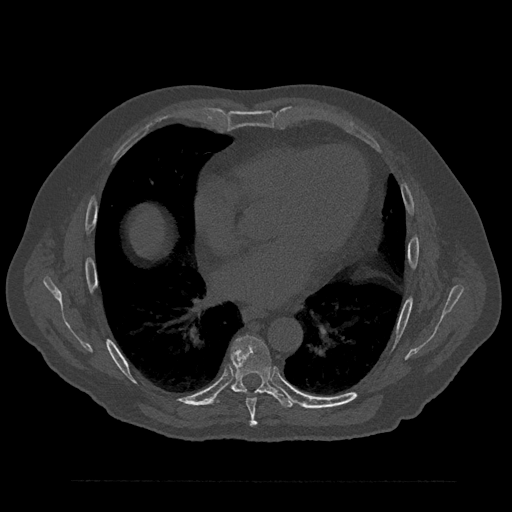
CT including the spine, one axial slice; slice 477 of 797 in the series (ordered by position); 120 kVp; bone window (W 1800 / L 400 HU); 0.5 mm slice thickness; 512 × 512 image matrix. Patient: male, 61 years. Case-level facts recorded for this patient, not image findings: primary cancer: prostate.
Structures marked on this image (semi-automatically segmented with operator editing):
- T7 vertebra: bounding box <241,391,259,426> (left, top, right, bottom; pixels)
- T8 vertebra: <217,335,295,408>